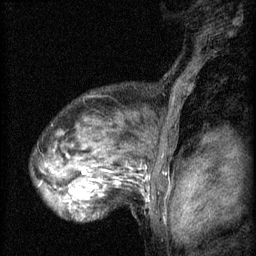
Breast MRI (dynamic contrast-enhanced), one sagittal slice; position 47 of 60 along the scan axis; 3 images stored at this slice position (order not interpretable as contrast timing); 1.5 T; TE 4.2 ms, TR 8.2 ms; 2 mm slice thickness; 256 × 256 image matrix, field of view 180 × 180 mm. Female patient, age 48 years.
Annotated regions visible in this slice (semi-automatically segmented with operator editing):
- analysis volume of interest (the breast-tissue region the enhancement analysis was run in; not a lesion): bounding box (x1, y1, x2, y2) in pixels: (48, 160, 125, 217)
- tumour enhancement mask (voxels above the 70 % enhancement threshold inside the analysis volume of interest): (64, 170, 120, 209)